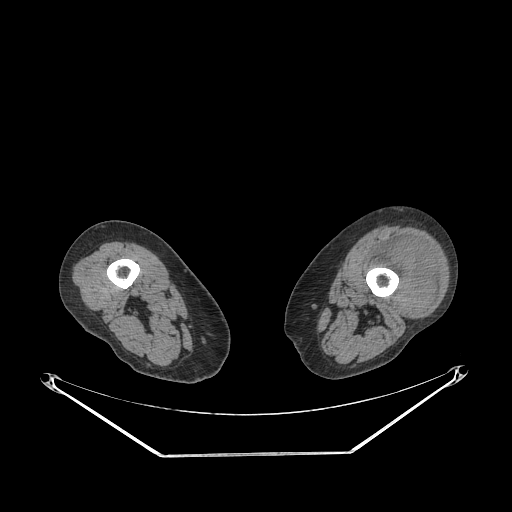
CT of an extremity soft-tissue mass (from a PET/CT study), one axial slice; position 205 of 267 along the scan axis; reconstruction kernel STANDARD; 140 kVp; soft-tissue window (W 400 / L 40 HU); 3.75 mm slice thickness; 512 × 512 image matrix, field of view 500 × 500 mm. Female patient. Case-level facts recorded for this patient, not image findings: histological type: undifferentiated – high grade; grade: high; site of the primary tumour: left thigh.
Annotated regions visible in this slice (expert contour drawn on MRI and transferred to this co-registered scan by the dataset authors):
- gross tumour volume including surrounding oedema: bounding box [x1, y1, x2, y2] px = [368, 237, 437, 314]
- gross tumour volume (mass): [393, 244, 437, 314]